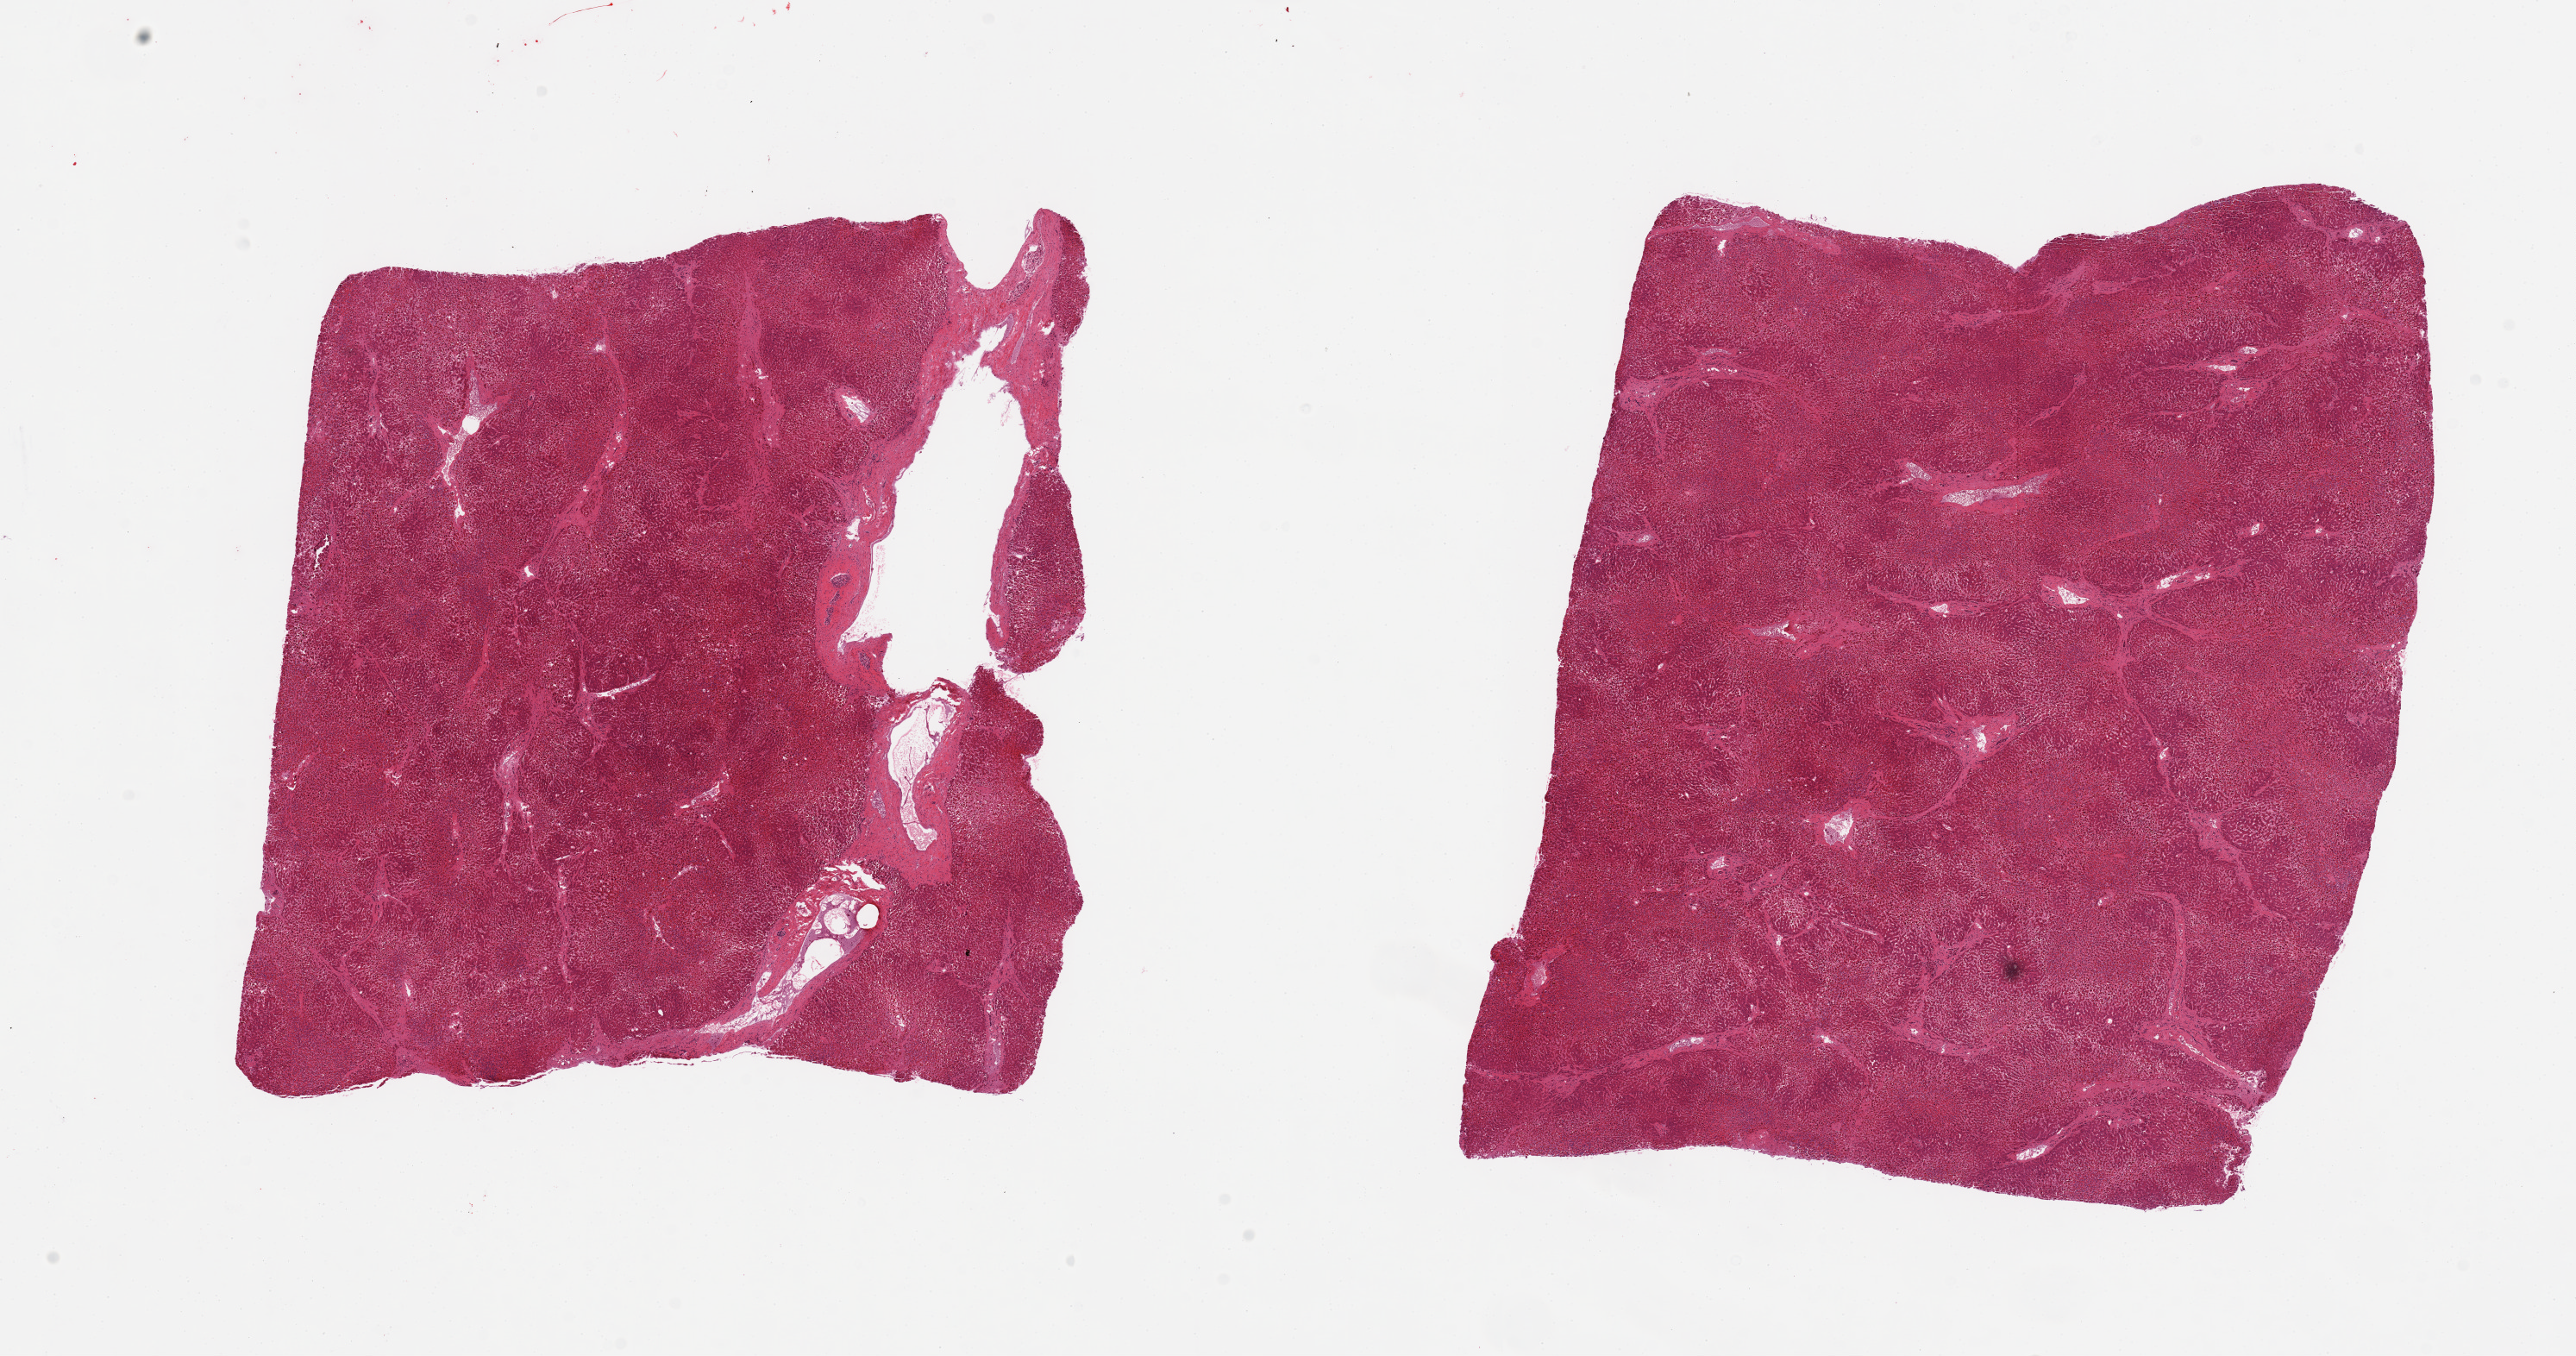
H&E whole-slide image, shown as a low-resolution overview of the whole scanned area (about 23.6 x 12.4 mm, slide scanned at 20x); PAXgene-fixed paraffin-embedded (PFPE) section; sampled site (target tissue): liver; donor tissue sample. Male donor.
Review note (as recorded): 2 pieces; acute necrosis centrally with polymorphs.